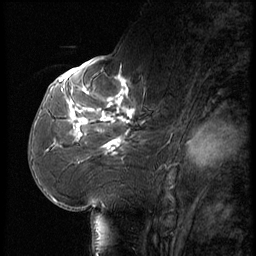
Breast MRI (dynamic contrast-enhanced), one sagittal slice; slice 30 of 56 in the series (ordered by position); dynamic contrast-enhanced series, image 2 of 3 at this slice position (ordered by acquisition); 1.5 T; TE 4.2 ms, TR 9 ms; 2.5 mm slice thickness; 256 × 256 image matrix, field of view 180 × 180 mm. Patient: female, 61 years. From the clinical record (not read from this slice): setting: breast cancer imaged before/during neoadjuvant chemotherapy; receptor status: HR-positive, HER2-negative.
Annotated regions visible in this slice (semi-automatically segmented with operator editing):
- analysis volume of interest (the breast-tissue region the enhancement analysis was run in; not a lesion): bounding box [x1, y1, x2, y2] px = [65, 74, 164, 175]
- tumour enhancement mask (voxels above the 140 % enhancement threshold inside the analysis volume of interest): [71, 78, 136, 154]